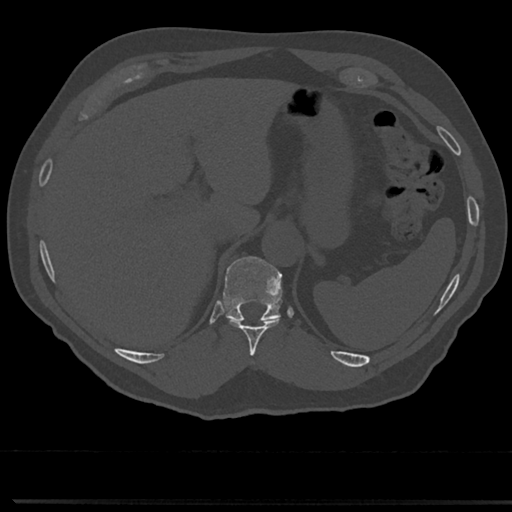
CT including the spine, one axial slice; reconstruction kernel Br40s/3; bone window (W 1800 / L 400 HU); 512 × 512 image matrix. Male patient, age 61 years. Case-level facts recorded for this patient, not image findings: primary cancer: prostate.
Structures marked on this image (semi-automatic segmentation, software-assisted and operator-edited):
- T10 vertebra: bounding box [x1, y1, x2, y2] px = [227, 317, 281, 354]
- T11 vertebra: [224, 256, 281, 322]